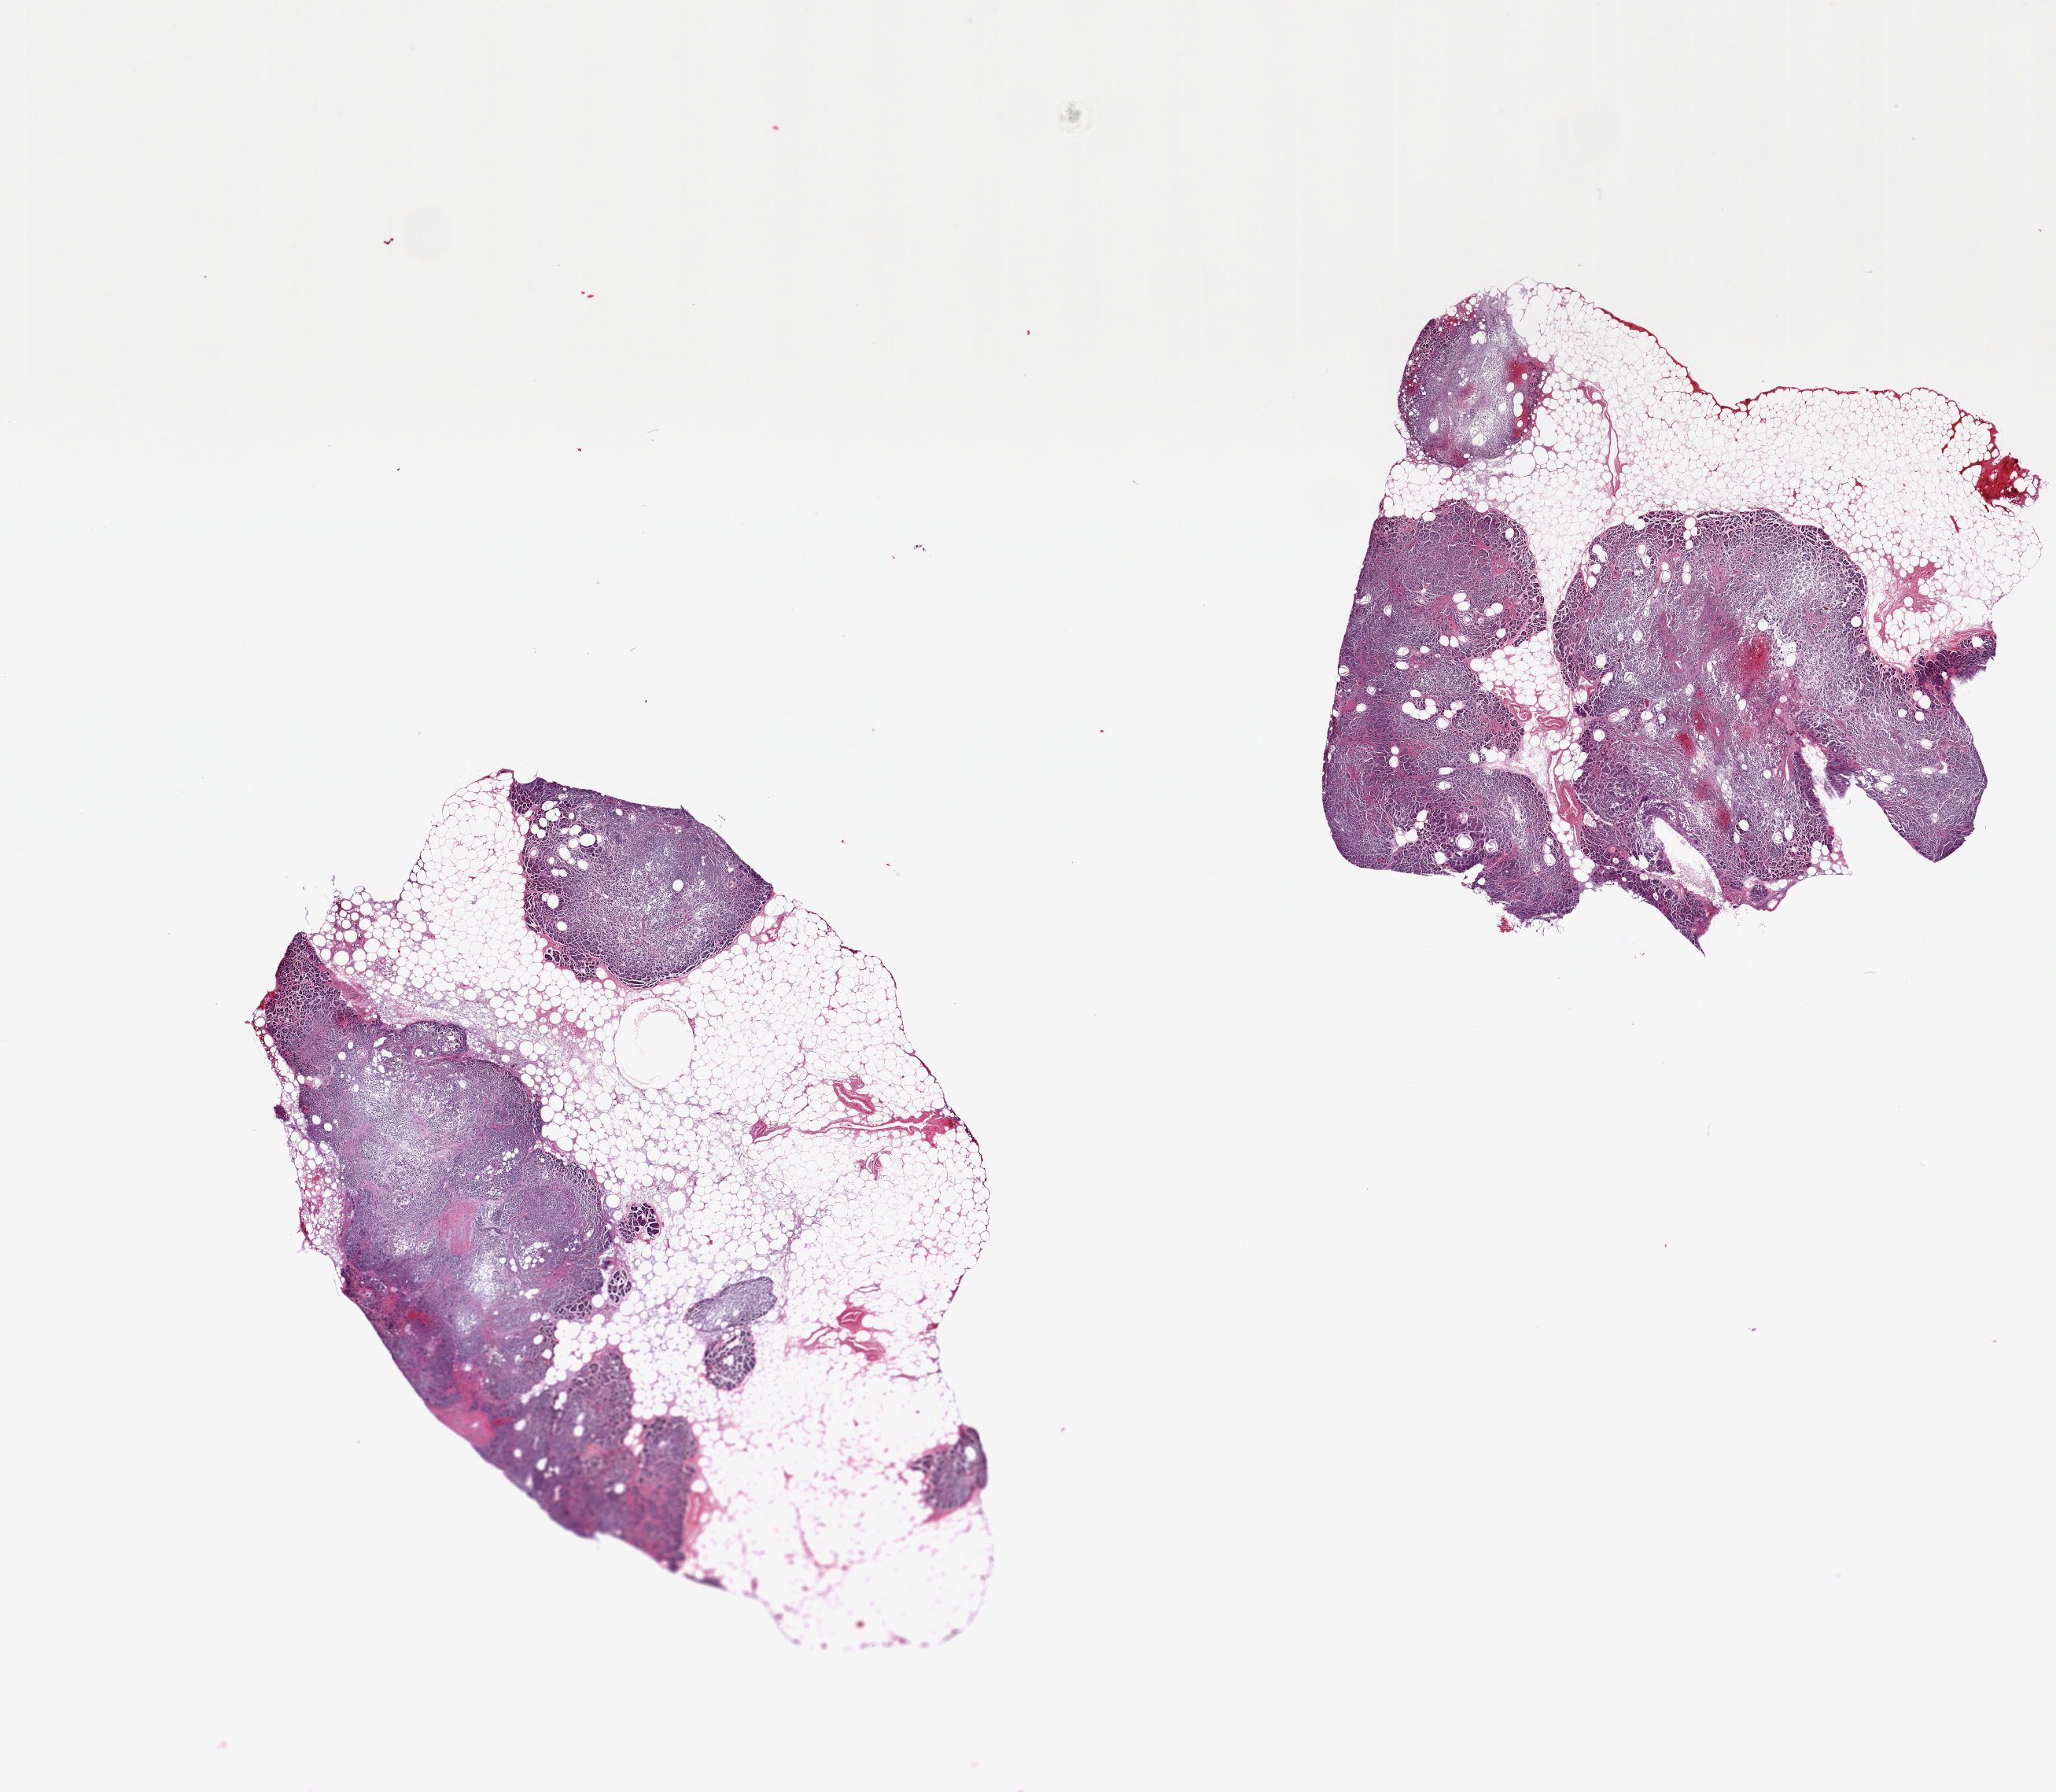
Whole-slide image, haematoxylin and eosin stain — a low-resolution overview of the entire scanned area, about 20.7 x 18.0 mm. PAXgene-fixed paraffin-embedded (PFPE) section. Target tissue: pancreas. Donor tissue sample. Female donor.
Reviewer comment on this tissue sample: 2 pieces, one with 30% other with 50% fat.